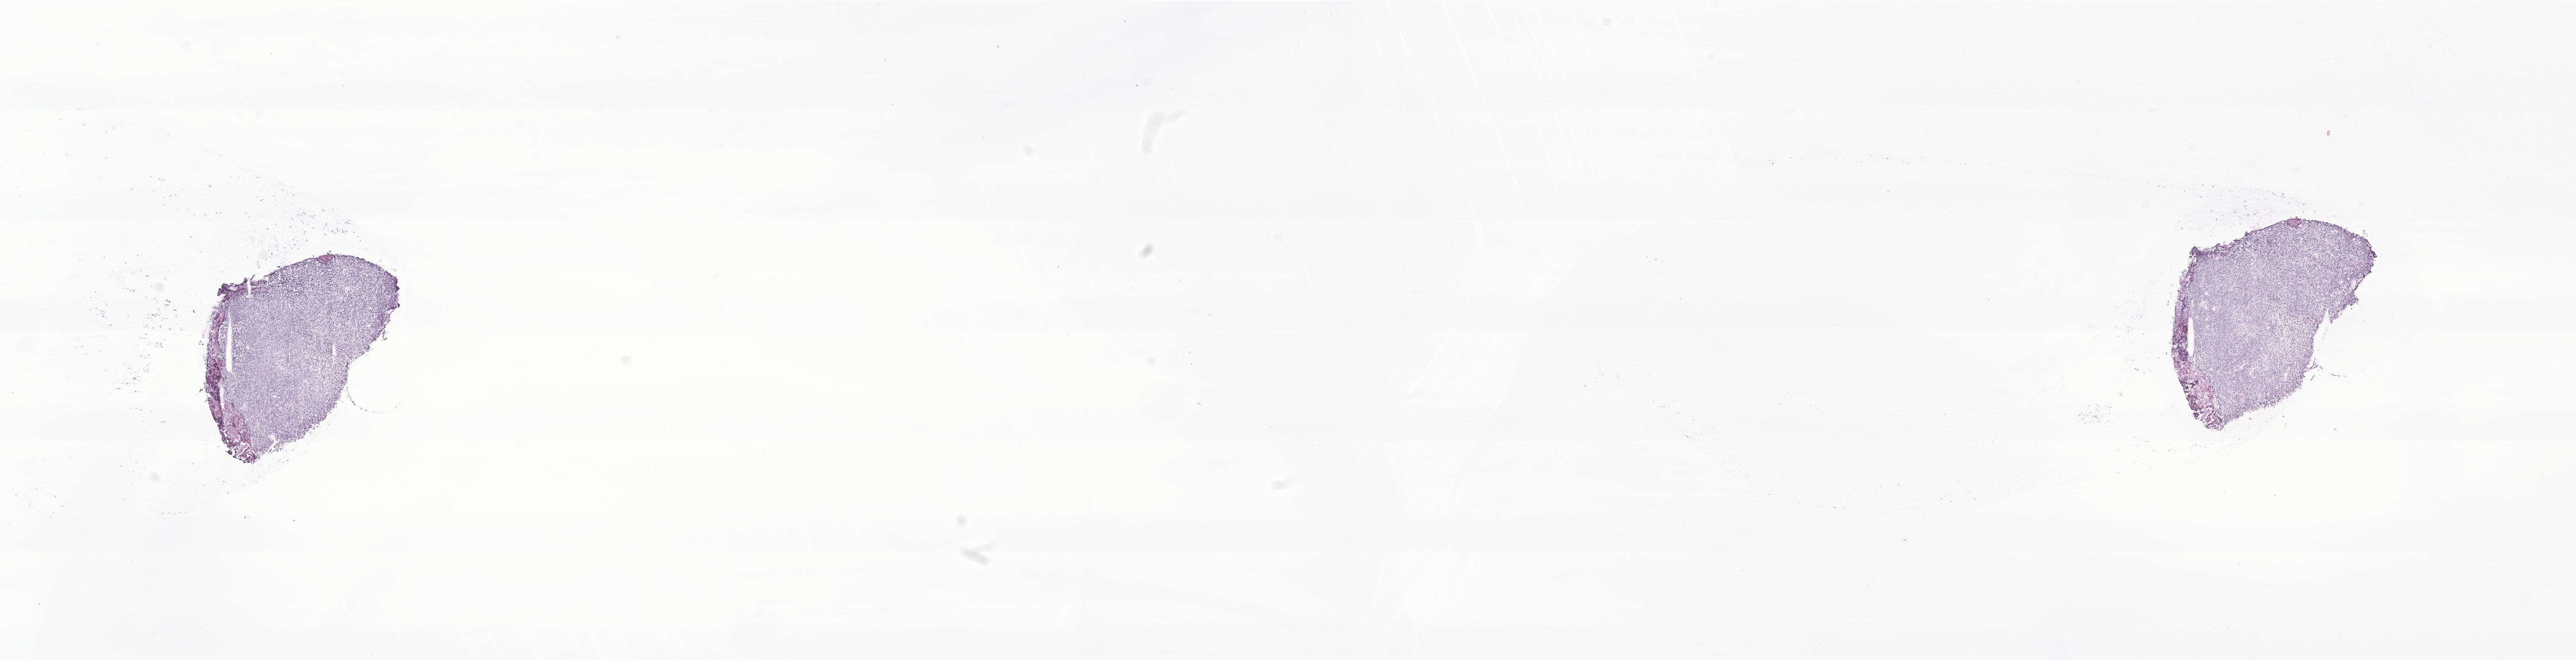
Hematoxylin and eosin (H&E) whole-slide image of tumor tissue from the brain — low-resolution overview of the scanned area, about 25.0 x 6.4 mm; frozen section. Male patient, age 108 months (9 years).
Diagnosis: Medulloblastoma, NOS.